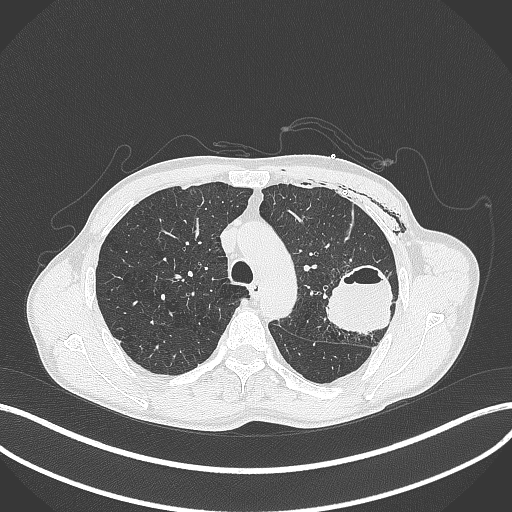
Chest CT, one axial slice; position 293 of 457 along the scan axis; reconstruction kernel B70f; lung window (W 1500 / L -600 HU); 1 mm slice thickness; 512 × 512 image matrix, field of view 400 × 400 mm. Patient: male, 58 years. From the clinical record (not read from this slice): clinical TNM (as recorded): T3 N0 M0.
Annotated regions visible in this slice (rectangle marked by the reading radiologist):
- lung tumour (recorded histology: adenocarcinoma): bounding box <324,258,395,341> (left, top, right, bottom; pixels)